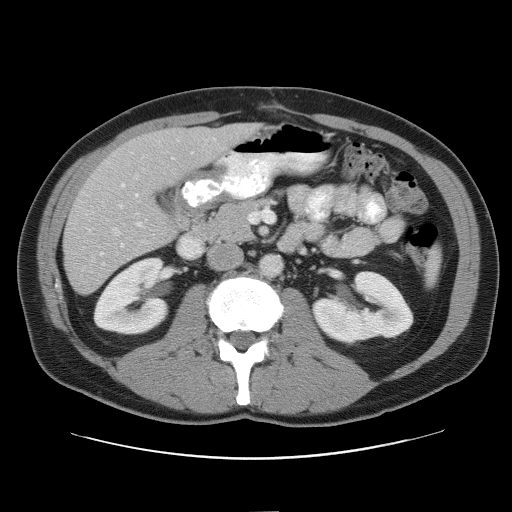
Contrast-enhanced abdominal CT, one axial slice; position 26 of 52 along the scan axis; intravenous contrast given; soft-tissue window (W 400 / L 40 HU); 512 × 512 image matrix. Male patient, age 70 years. Case-level facts recorded for this patient, not image findings: diagnosis: colorectal cancer liver metastases, imaged before liver resection; multiple liver metastases: yes.
Structures marked on this image (outlined manually by an expert reader):
- hepatic veins: bounding box <85,174,147,265> (left, top, right, bottom; pixels)
- liver: <64,124,257,294>
- planned liver remnant (the part of the liver to remain after resection): <118,124,257,190>
- portal vein (with intrahepatic branches): <119,182,144,227>